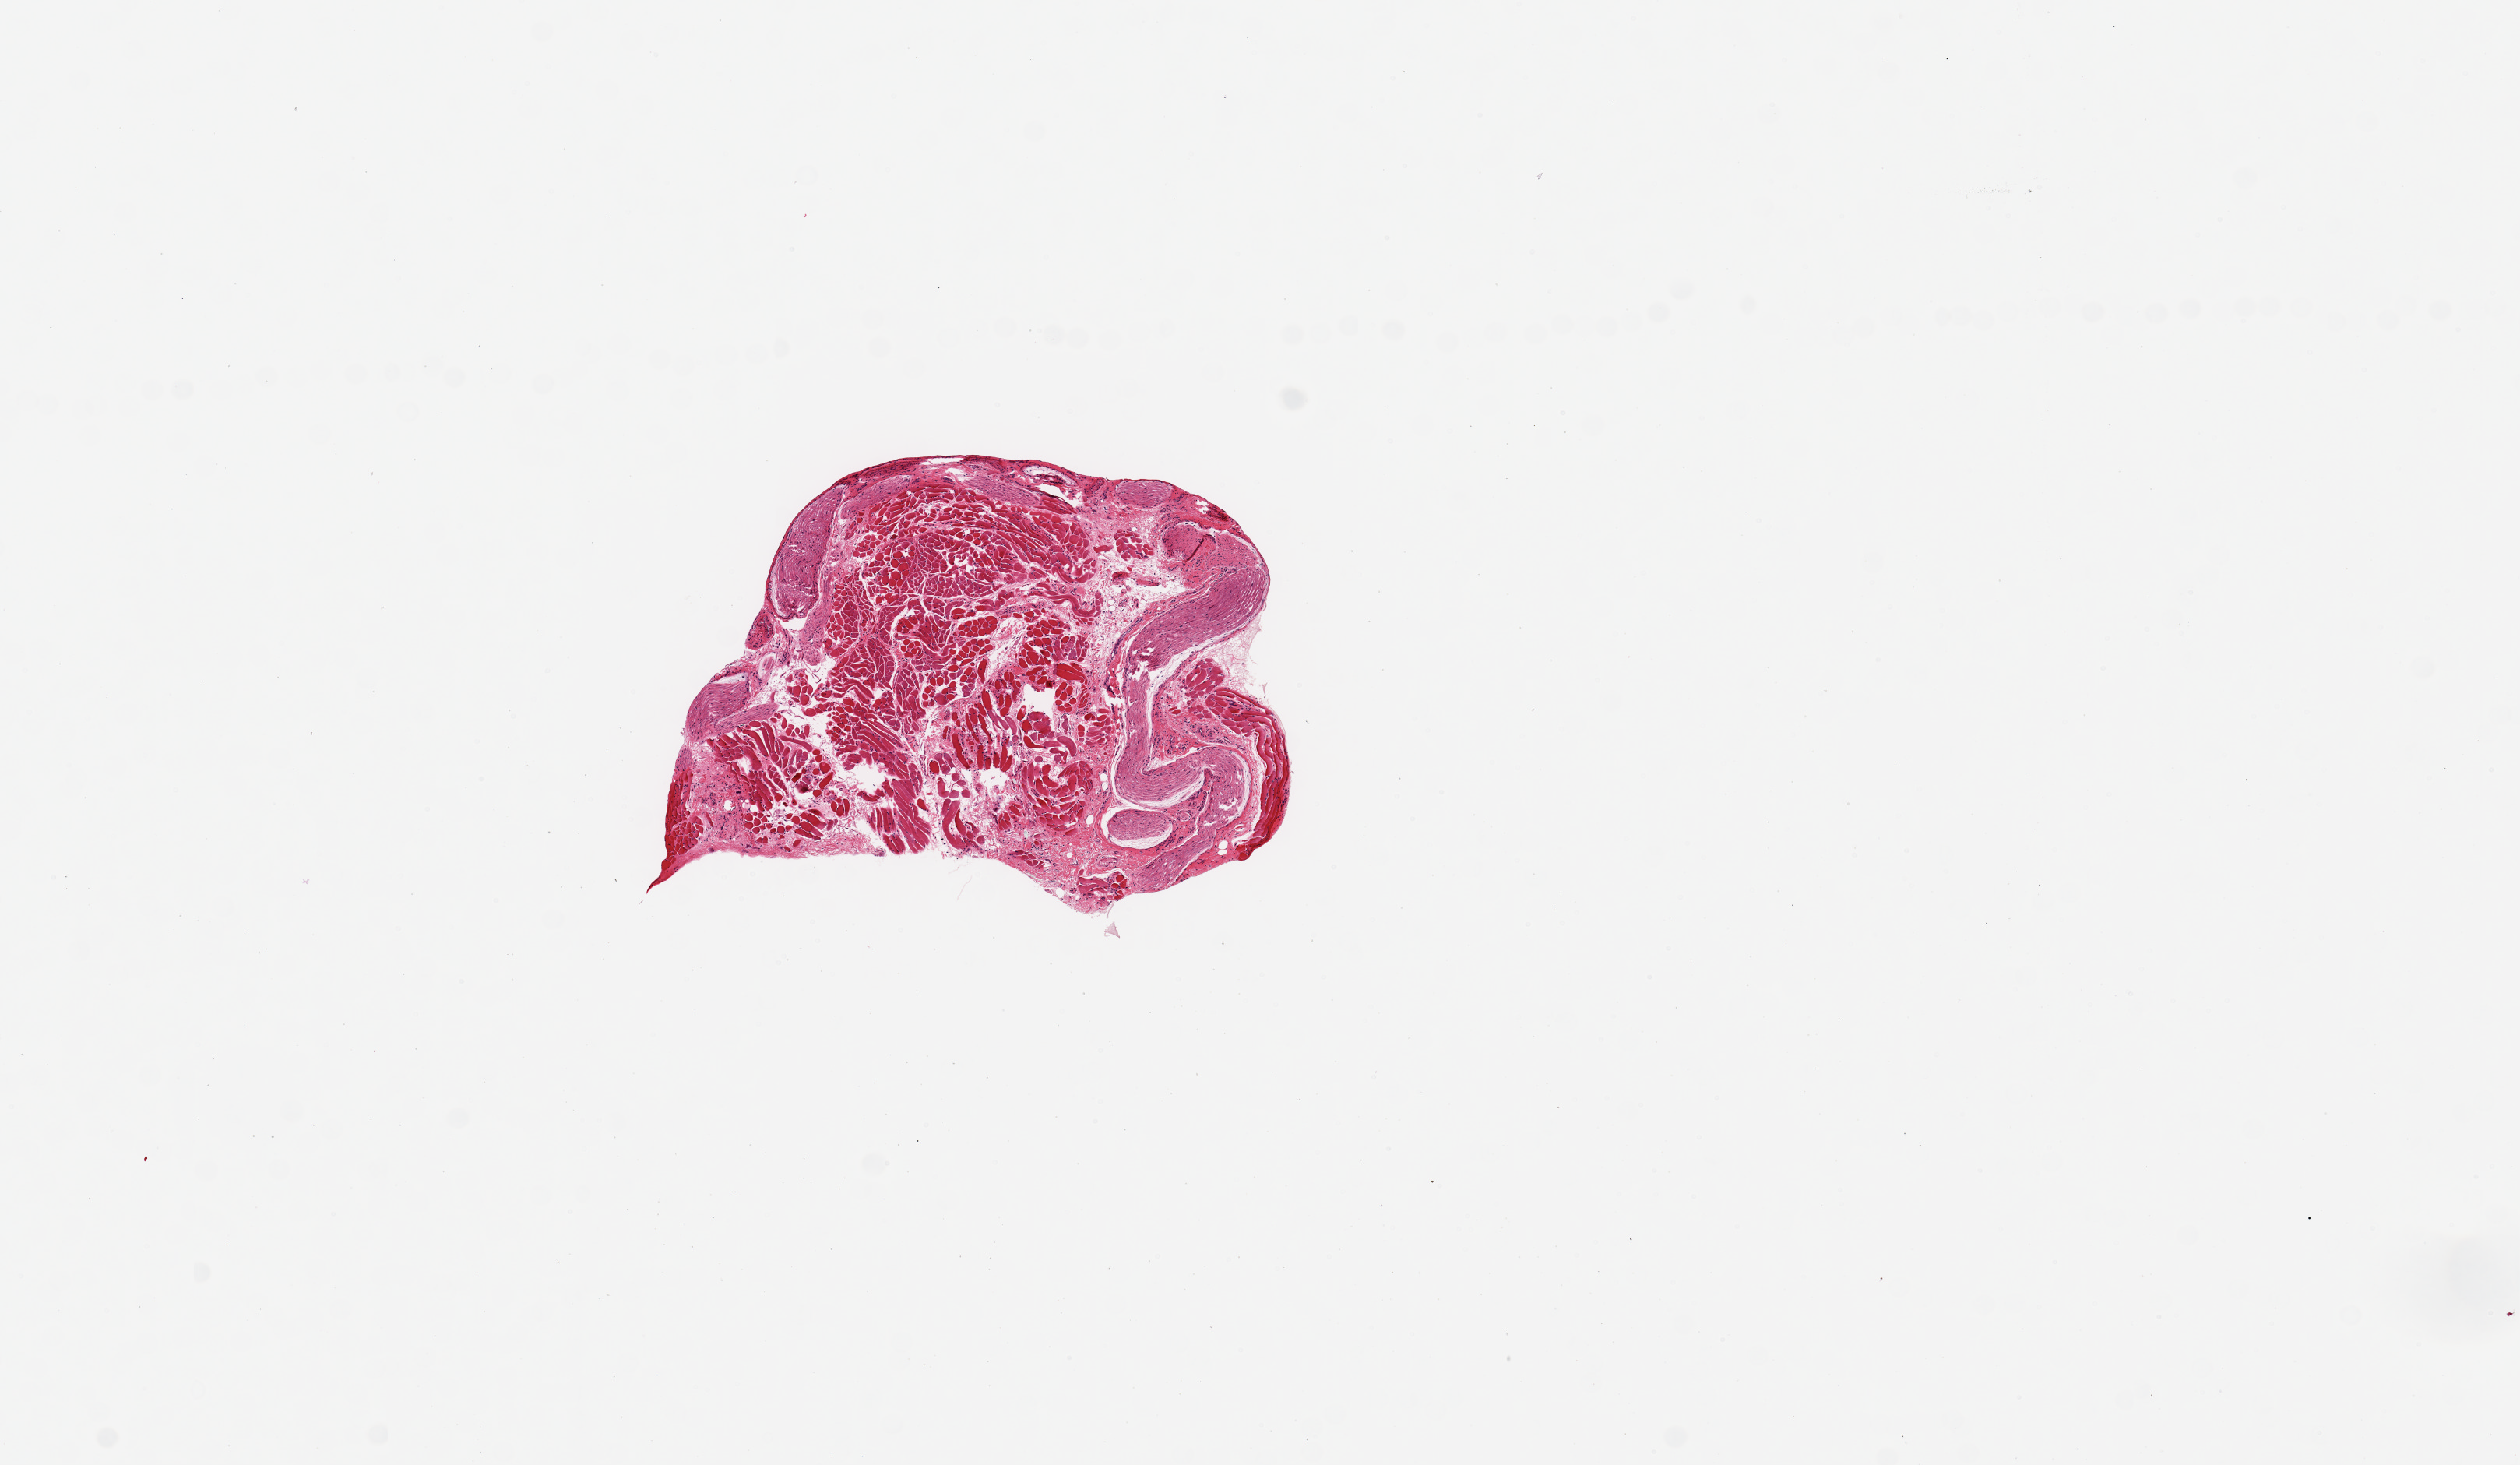
Haematoxylin and eosin whole-slide image, brightfield, low-resolution overview of the scanned area, about 12.8 x 7.4 mm. PAXgene-fixed paraffin-embedded (PFPE) section. Section of minor salivary gland (target tissue). Tissue donor sample. Donor: female.
Review note (as recorded): No salivary tissue present; nerve and muscle only.